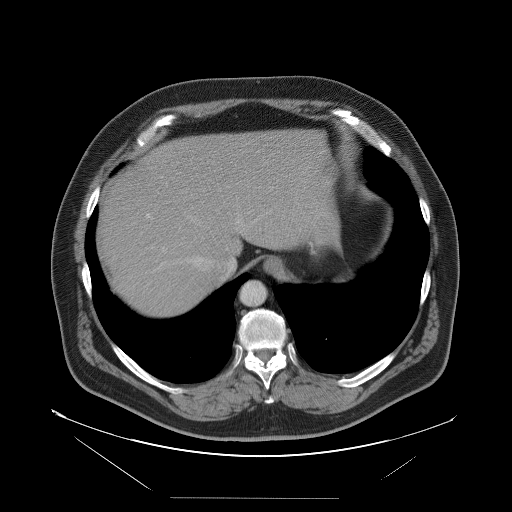
Contrast-enhanced abdominal CT, one axial slice; soft-tissue window (W 400 / L 40 HU); 5 mm slice thickness; 512 × 512 image matrix, field of view 500 × 500 mm. Male patient, age 61 years. Case-level facts recorded for this patient, not image findings: diagnosis: colorectal cancer liver metastases, imaged before liver resection; multiple liver metastases: no; largest metastasis: 6.5 cm; chemotherapy before resection: no.
Structures marked on this image (manually delineated by an expert):
- hepatic veins: bounding box <172,210,271,276> (left, top, right, bottom; pixels)
- liver: <97,129,321,320>
- planned liver remnant (the part of the liver to remain after resection): <149,129,322,283>